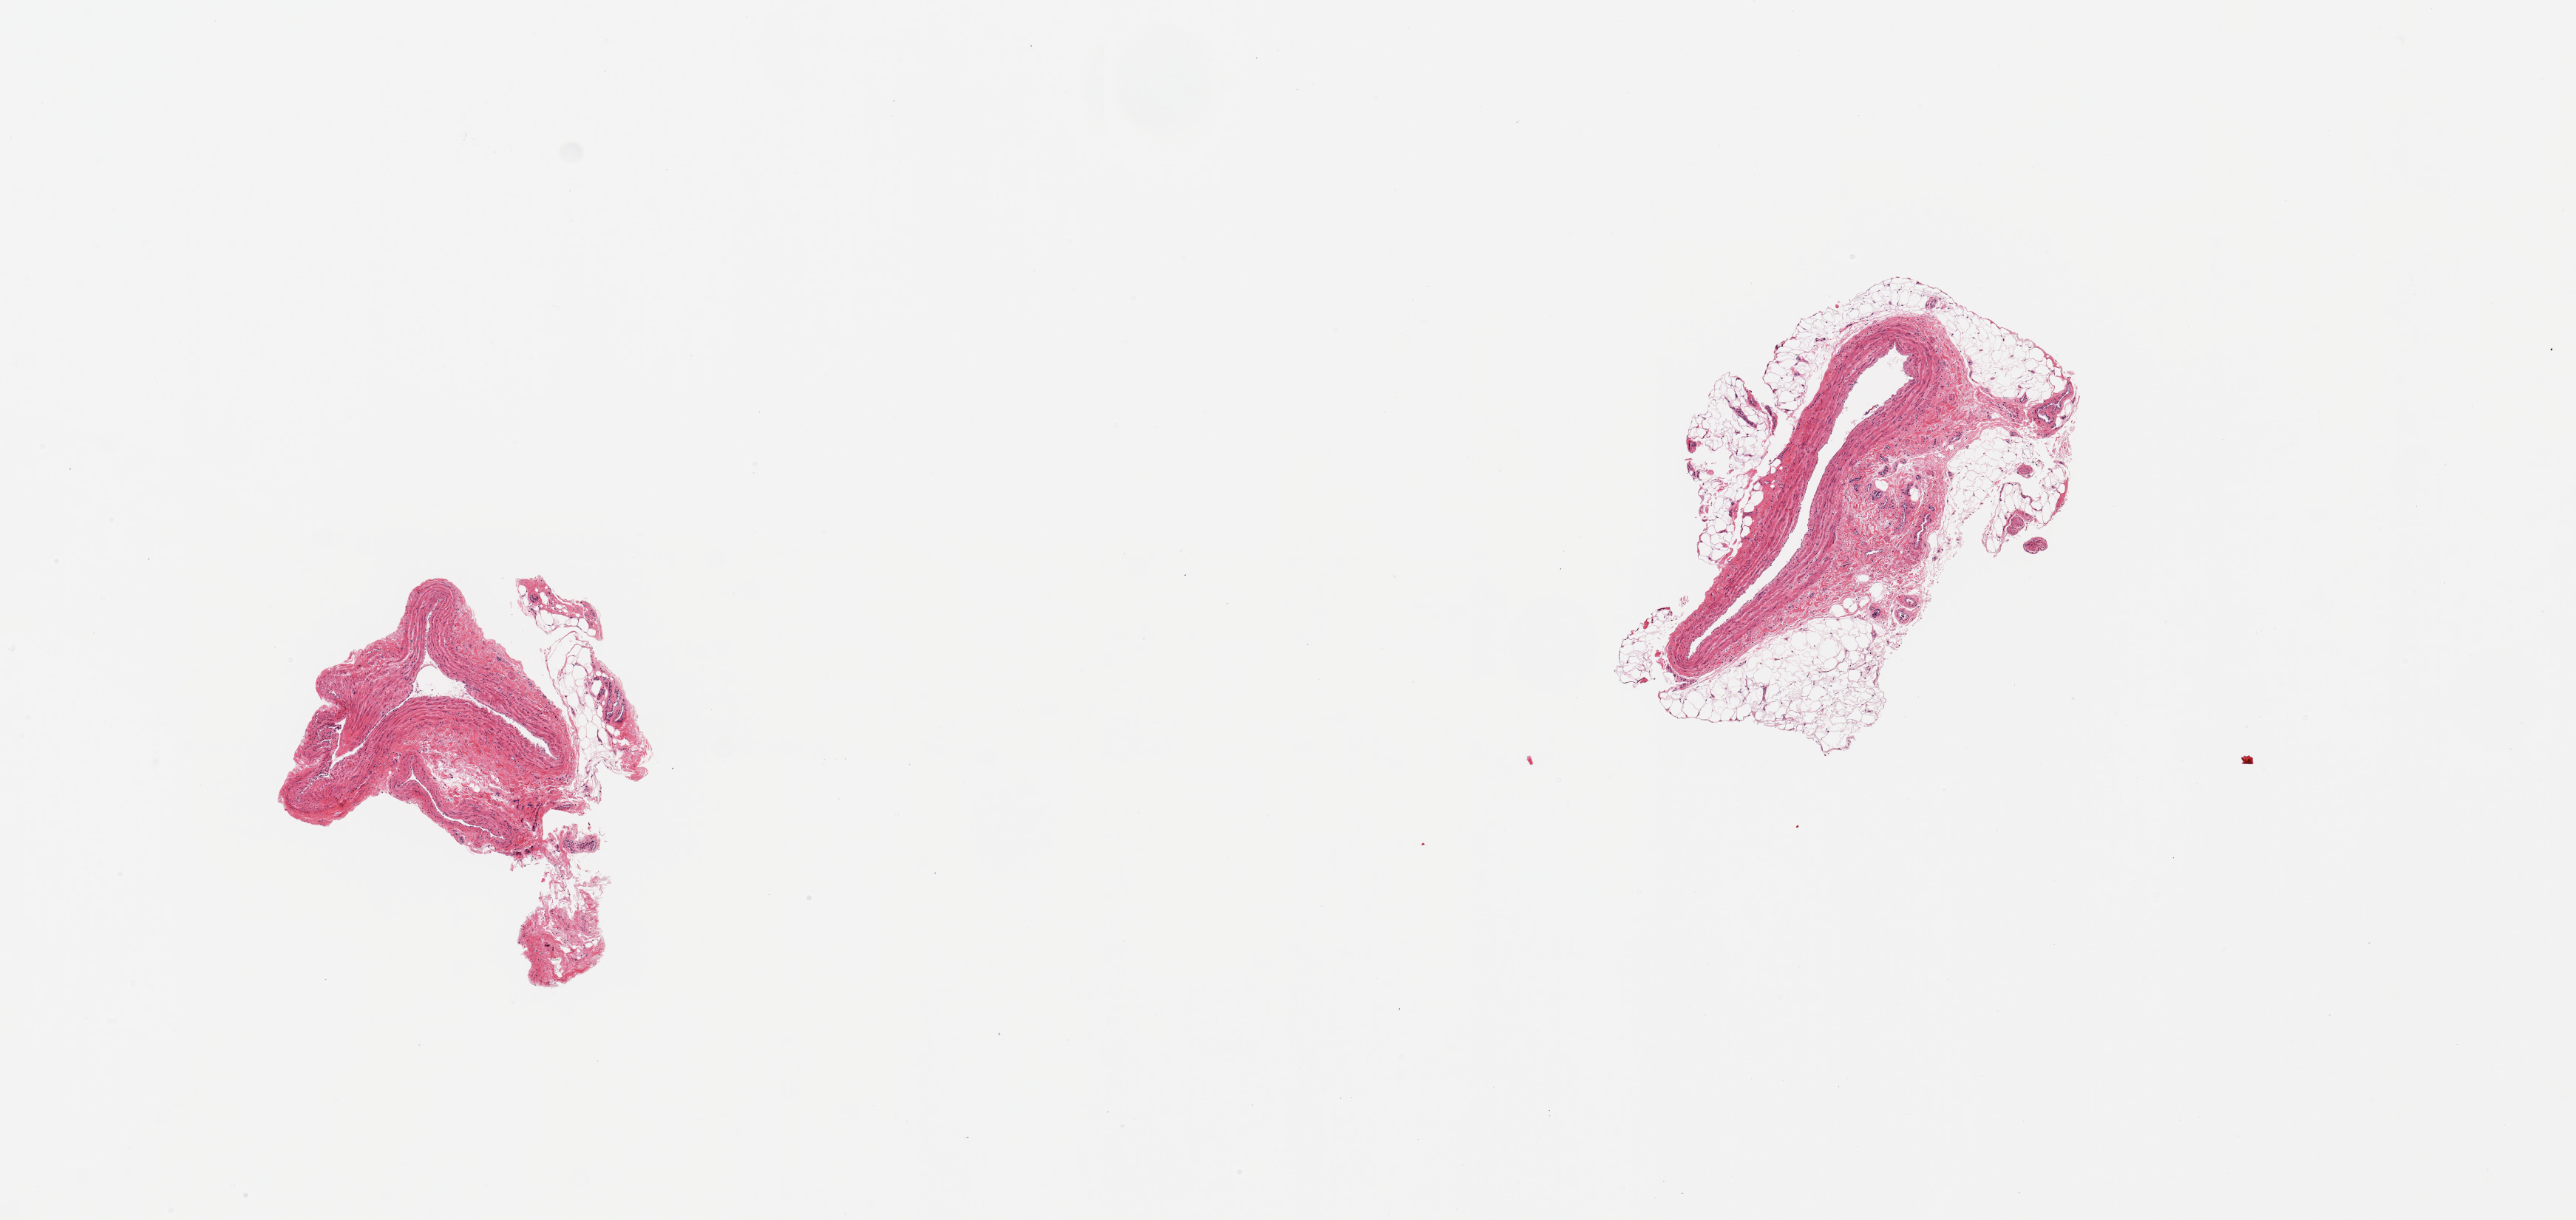
Haematoxylin and eosin whole-slide image, whole scanned area (about 13.8 x 6.5 mm, from a 20x scan) shown as a low-resolution overview. PAXgene-fixed paraffin-embedded (PFPE) section. Section of tibial nerve (target tissue). Donor tissue sample.
Pathologist's review note for this sample: 2 pieces NOT nerve; blood vessel.